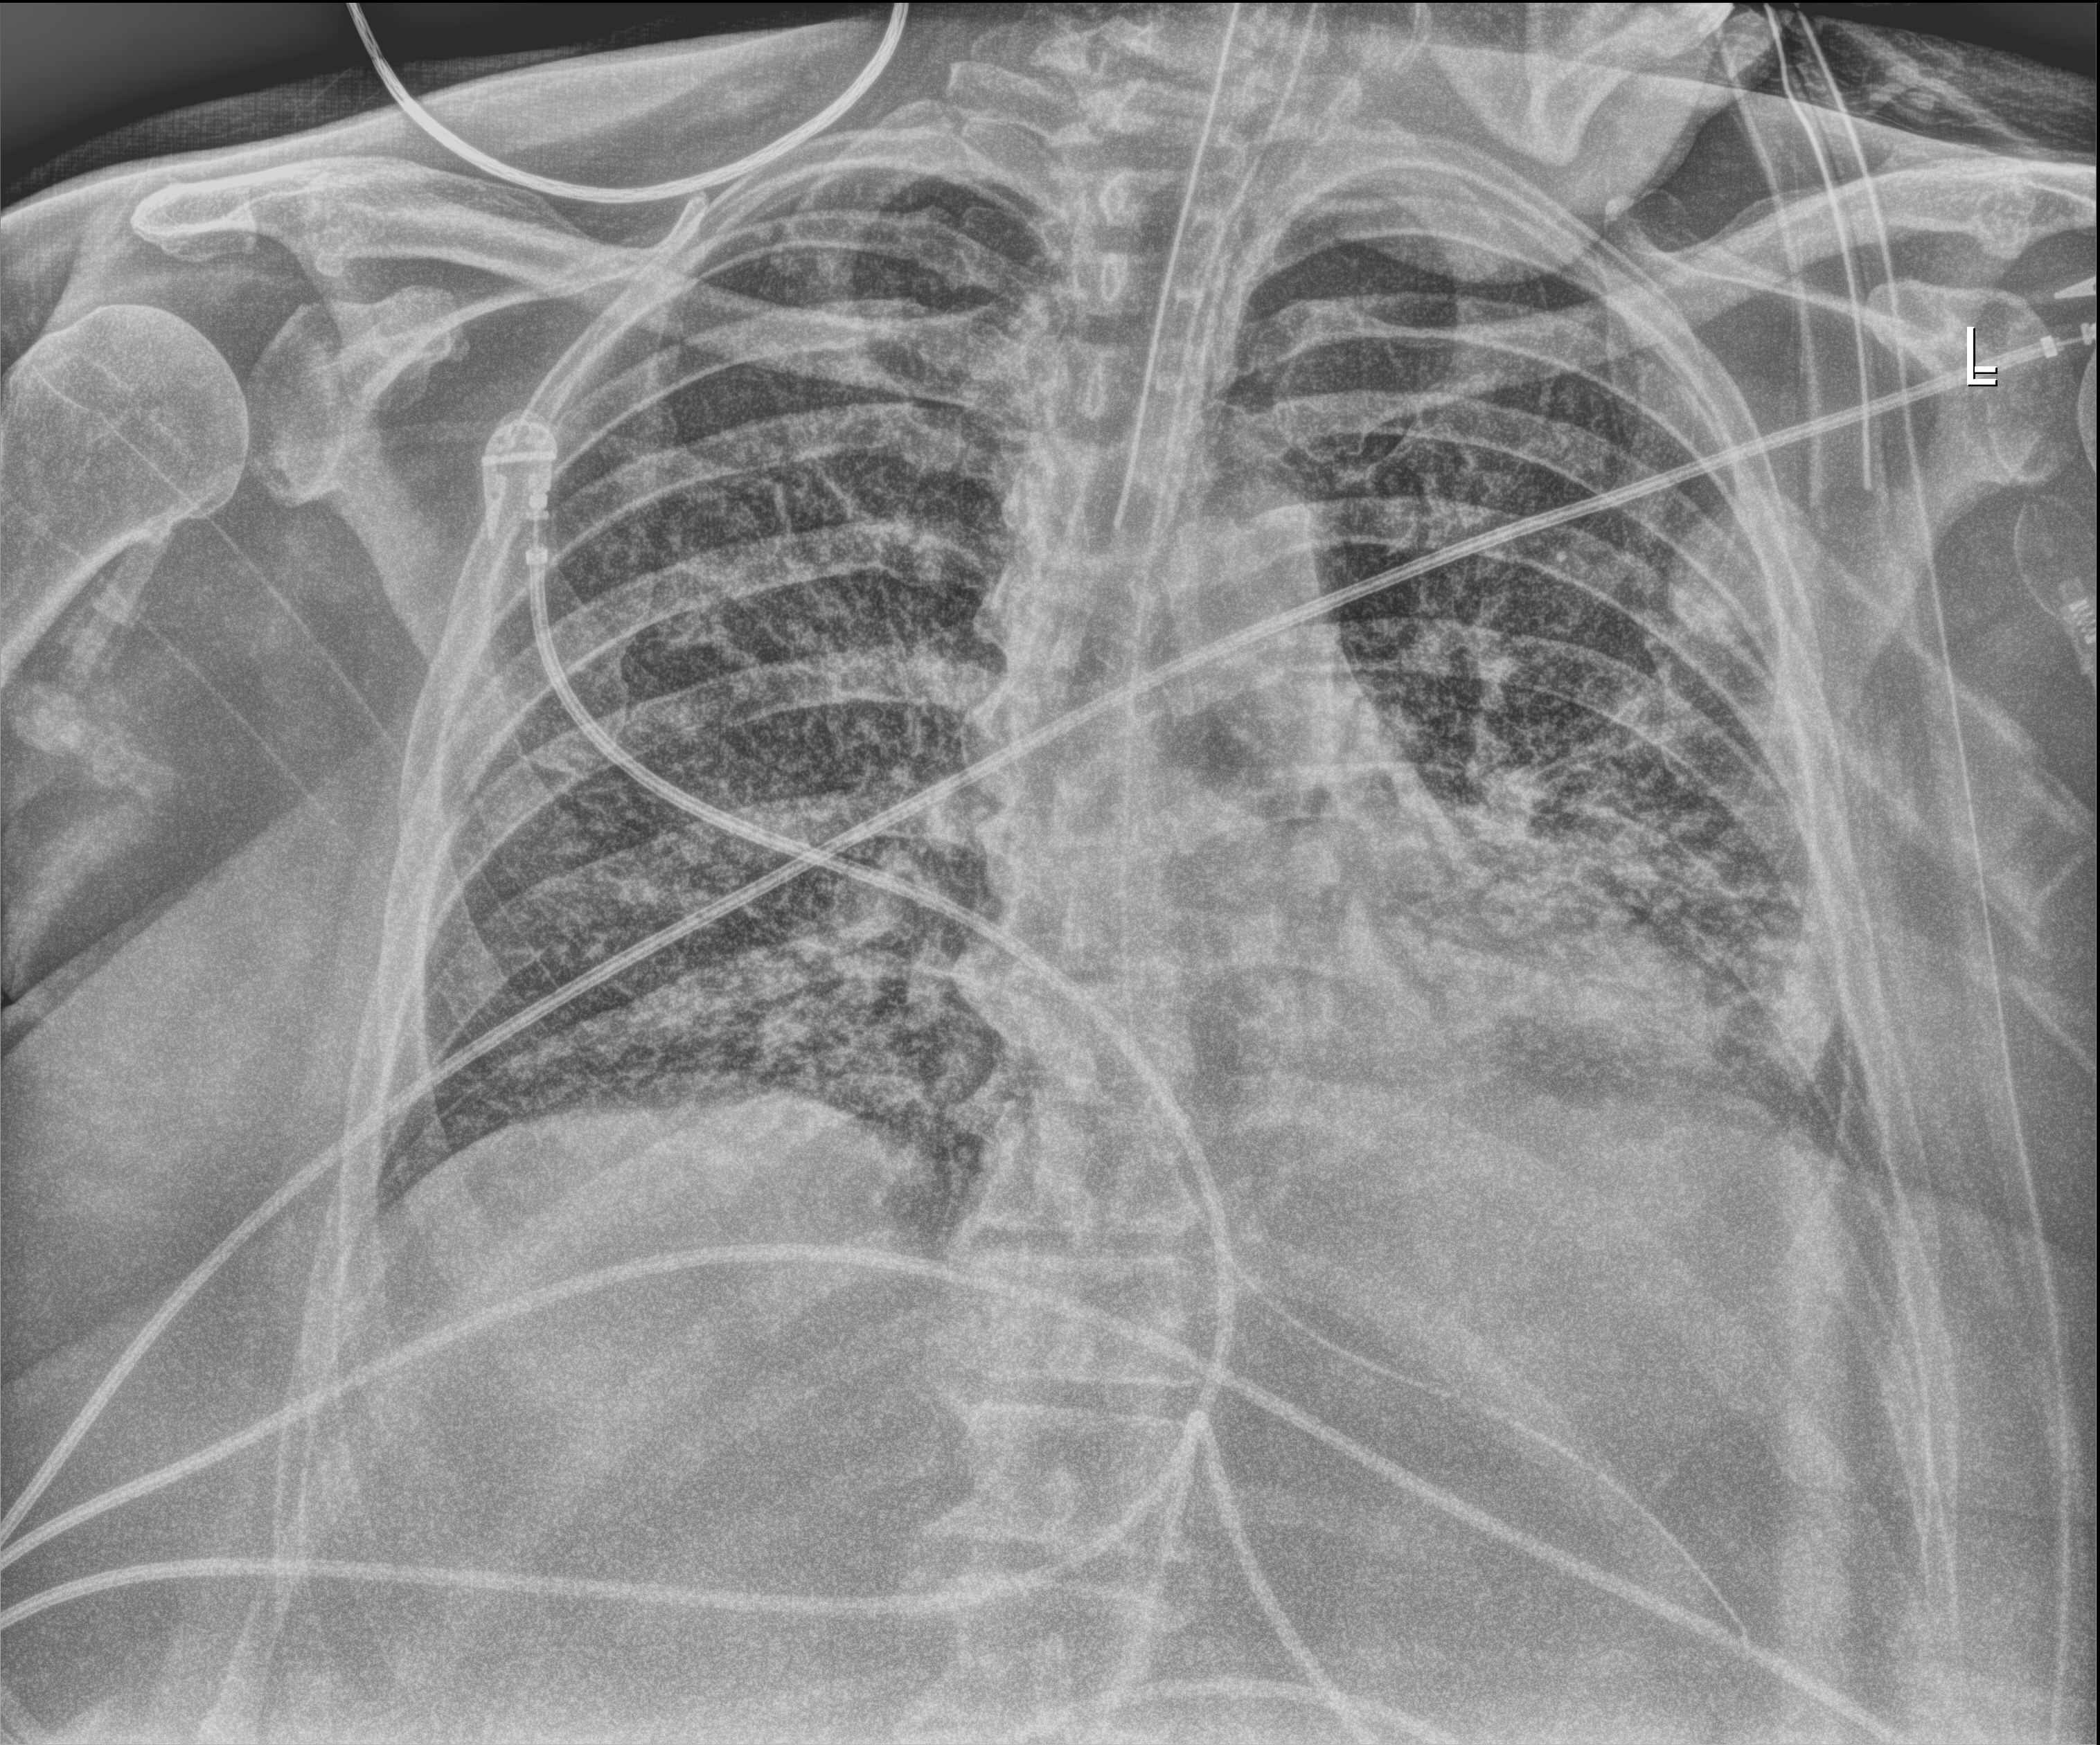
Chest radiograph (digital radiography), anteroposterior (AP) projection. Adult patient hospitalised with COVID-19, age 18–59 years.
From the hospital-stay record, not from the radiograph (when in the stay this image was taken is not recorded):
- mechanically ventilated during this hospital stay: yes
- admitted to intensive care during this hospital stay: yes
- length of hospital stay: 28 days